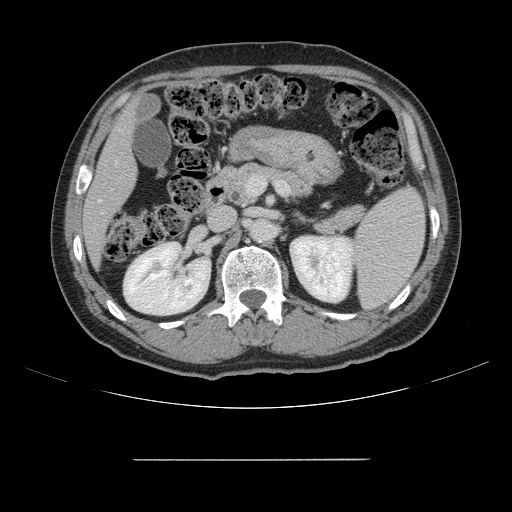
Contrast-enhanced abdominal CT, one axial slice. Position 71 of 164 along the scan axis. 120 kVp. Soft-tissue window (W 400 / L 40 HU). 2.5 mm slice thickness. 512 × 512 image matrix, field of view 404 × 404 mm. Male patient, age 54 years. From the clinical record (not read from this slice): diagnosis: colorectal cancer liver metastases, imaged before liver resection; multiple liver metastases: yes; largest metastasis: 1 cm; disease in both lobes: no.
Structures marked on this image (outlined manually by an expert reader):
- hepatic veins: box from (x=98, y=162) to (x=117, y=203) px
- liver: (x=85, y=107)–(x=136, y=261)
- planned liver remnant (the part of the liver to remain after resection): (x=85, y=107)–(x=136, y=262)